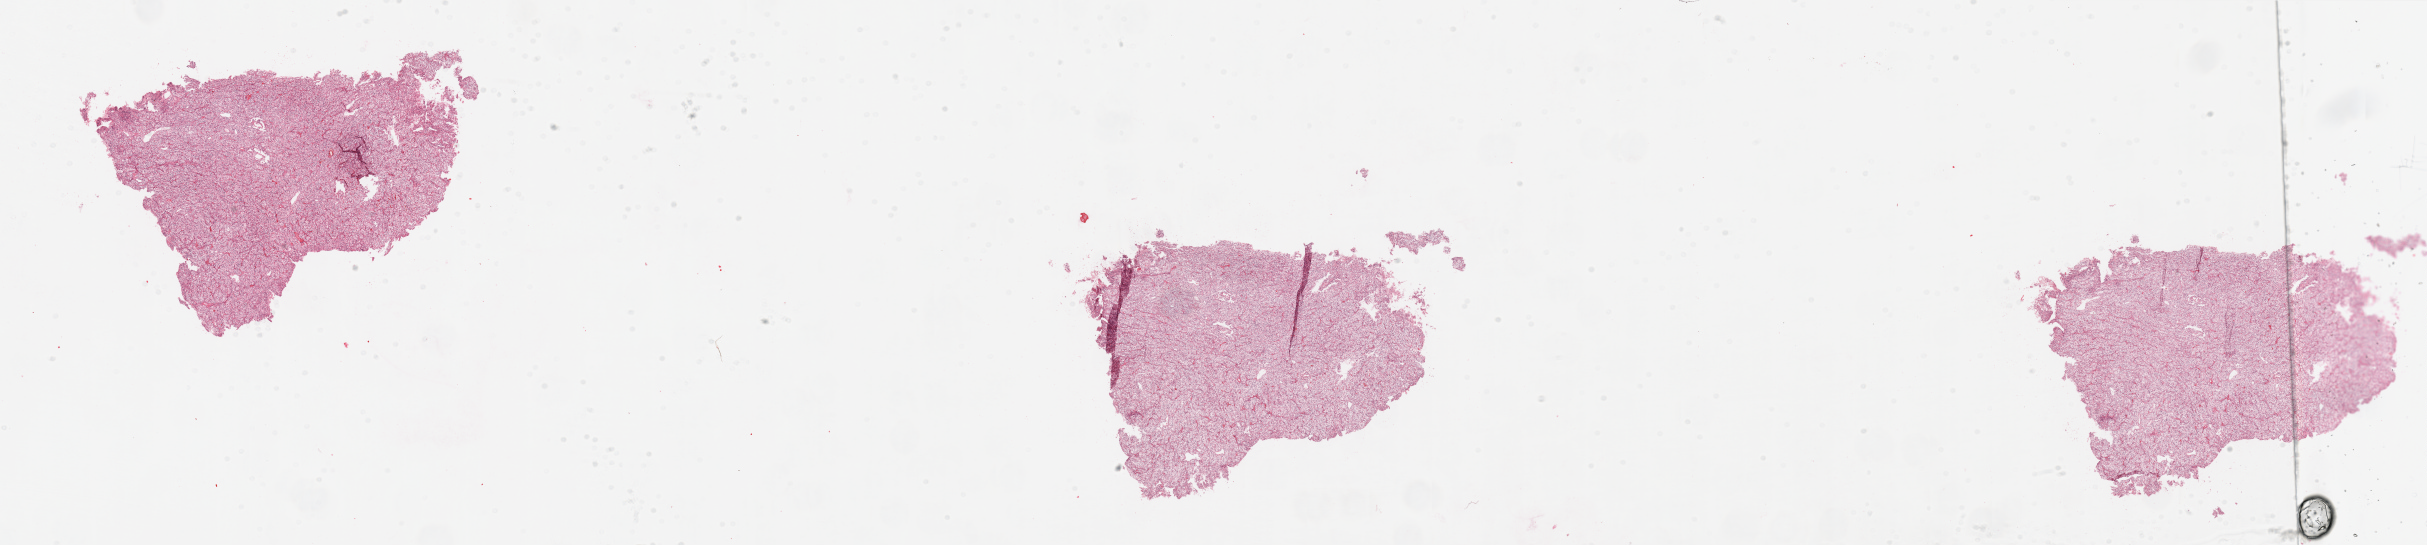
Digitized H&E tissue section (whole slide), a low-resolution overview of the entire scanned area, about 38.4 x 8.6 mm. Tumour tissue sample, sampled site: kidney. Male, 69 y/o.
Diagnosis: Renal cell carcinoma, NOS.